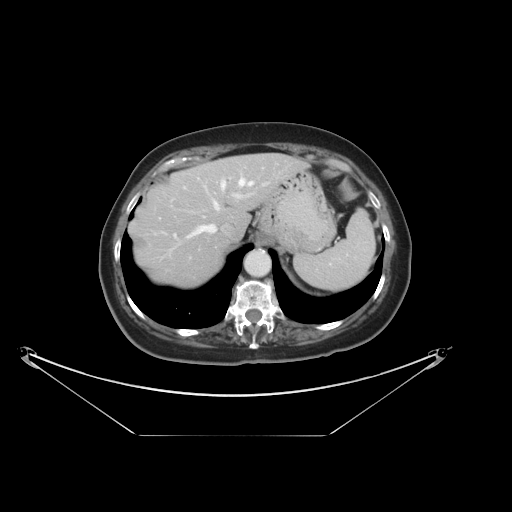
Contrast-enhanced abdominal CT, one axial slice. Slice 28 of 36 in the series (ordered by position). Reconstruction kernel STANDARD. 120 kVp. Soft-tissue window (W 400 / L 40 HU). 5 mm slice thickness. 512 × 512 image matrix, field of view 500 × 500 mm. Female patient, age 70 years. Case-level facts recorded for this patient, not image findings: diagnosis: colorectal cancer liver metastases, imaged before liver resection; multiple liver metastases: no; largest metastasis: 2.5 cm; disease in both lobes: no.
Annotated regions visible in this slice (manually delineated by an expert):
- hepatic veins: bounding box (x1, y1, x2, y2) in pixels: (188, 179, 253, 237)
- liver: (129, 154, 303, 287)
- planned liver remnant (the part of the liver to remain after resection): (129, 154, 304, 287)
- portal vein (with intrahepatic branches): (161, 181, 268, 239)